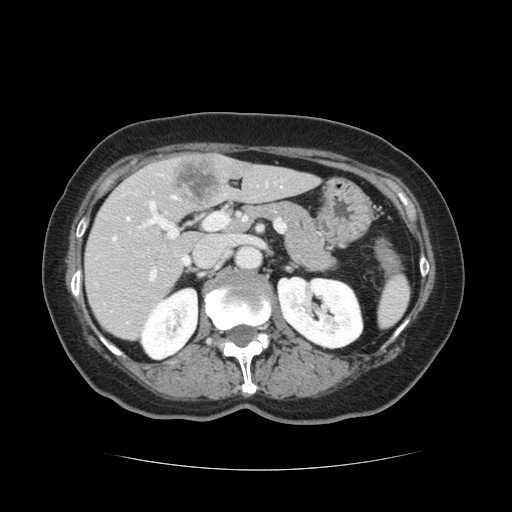
Contrast-enhanced abdominal CT, one axial slice; position 64 of 128 along the scan axis; 120 kVp; intravenous contrast given; soft-tissue window (W 400 / L 40 HU); 2.5 mm slice thickness; 512 × 512 image matrix. Female patient, age 67 years. From the clinical record (not read from this slice): diagnosis: colorectal cancer liver metastases, imaged before liver resection; multiple liver metastases: yes; largest metastasis: 3 cm; disease in both lobes: yes.
Outlined on this slice (outlined manually by an expert reader):
- hepatic veins: bounding box <114,196,188,263> (left, top, right, bottom; pixels)
- liver: <85,154,317,340>
- planned liver remnant (the part of the liver to remain after resection): <85,164,317,340>
- portal vein (with intrahepatic branches): <113,182,269,282>
- liver metastasis: <173,159,219,204>